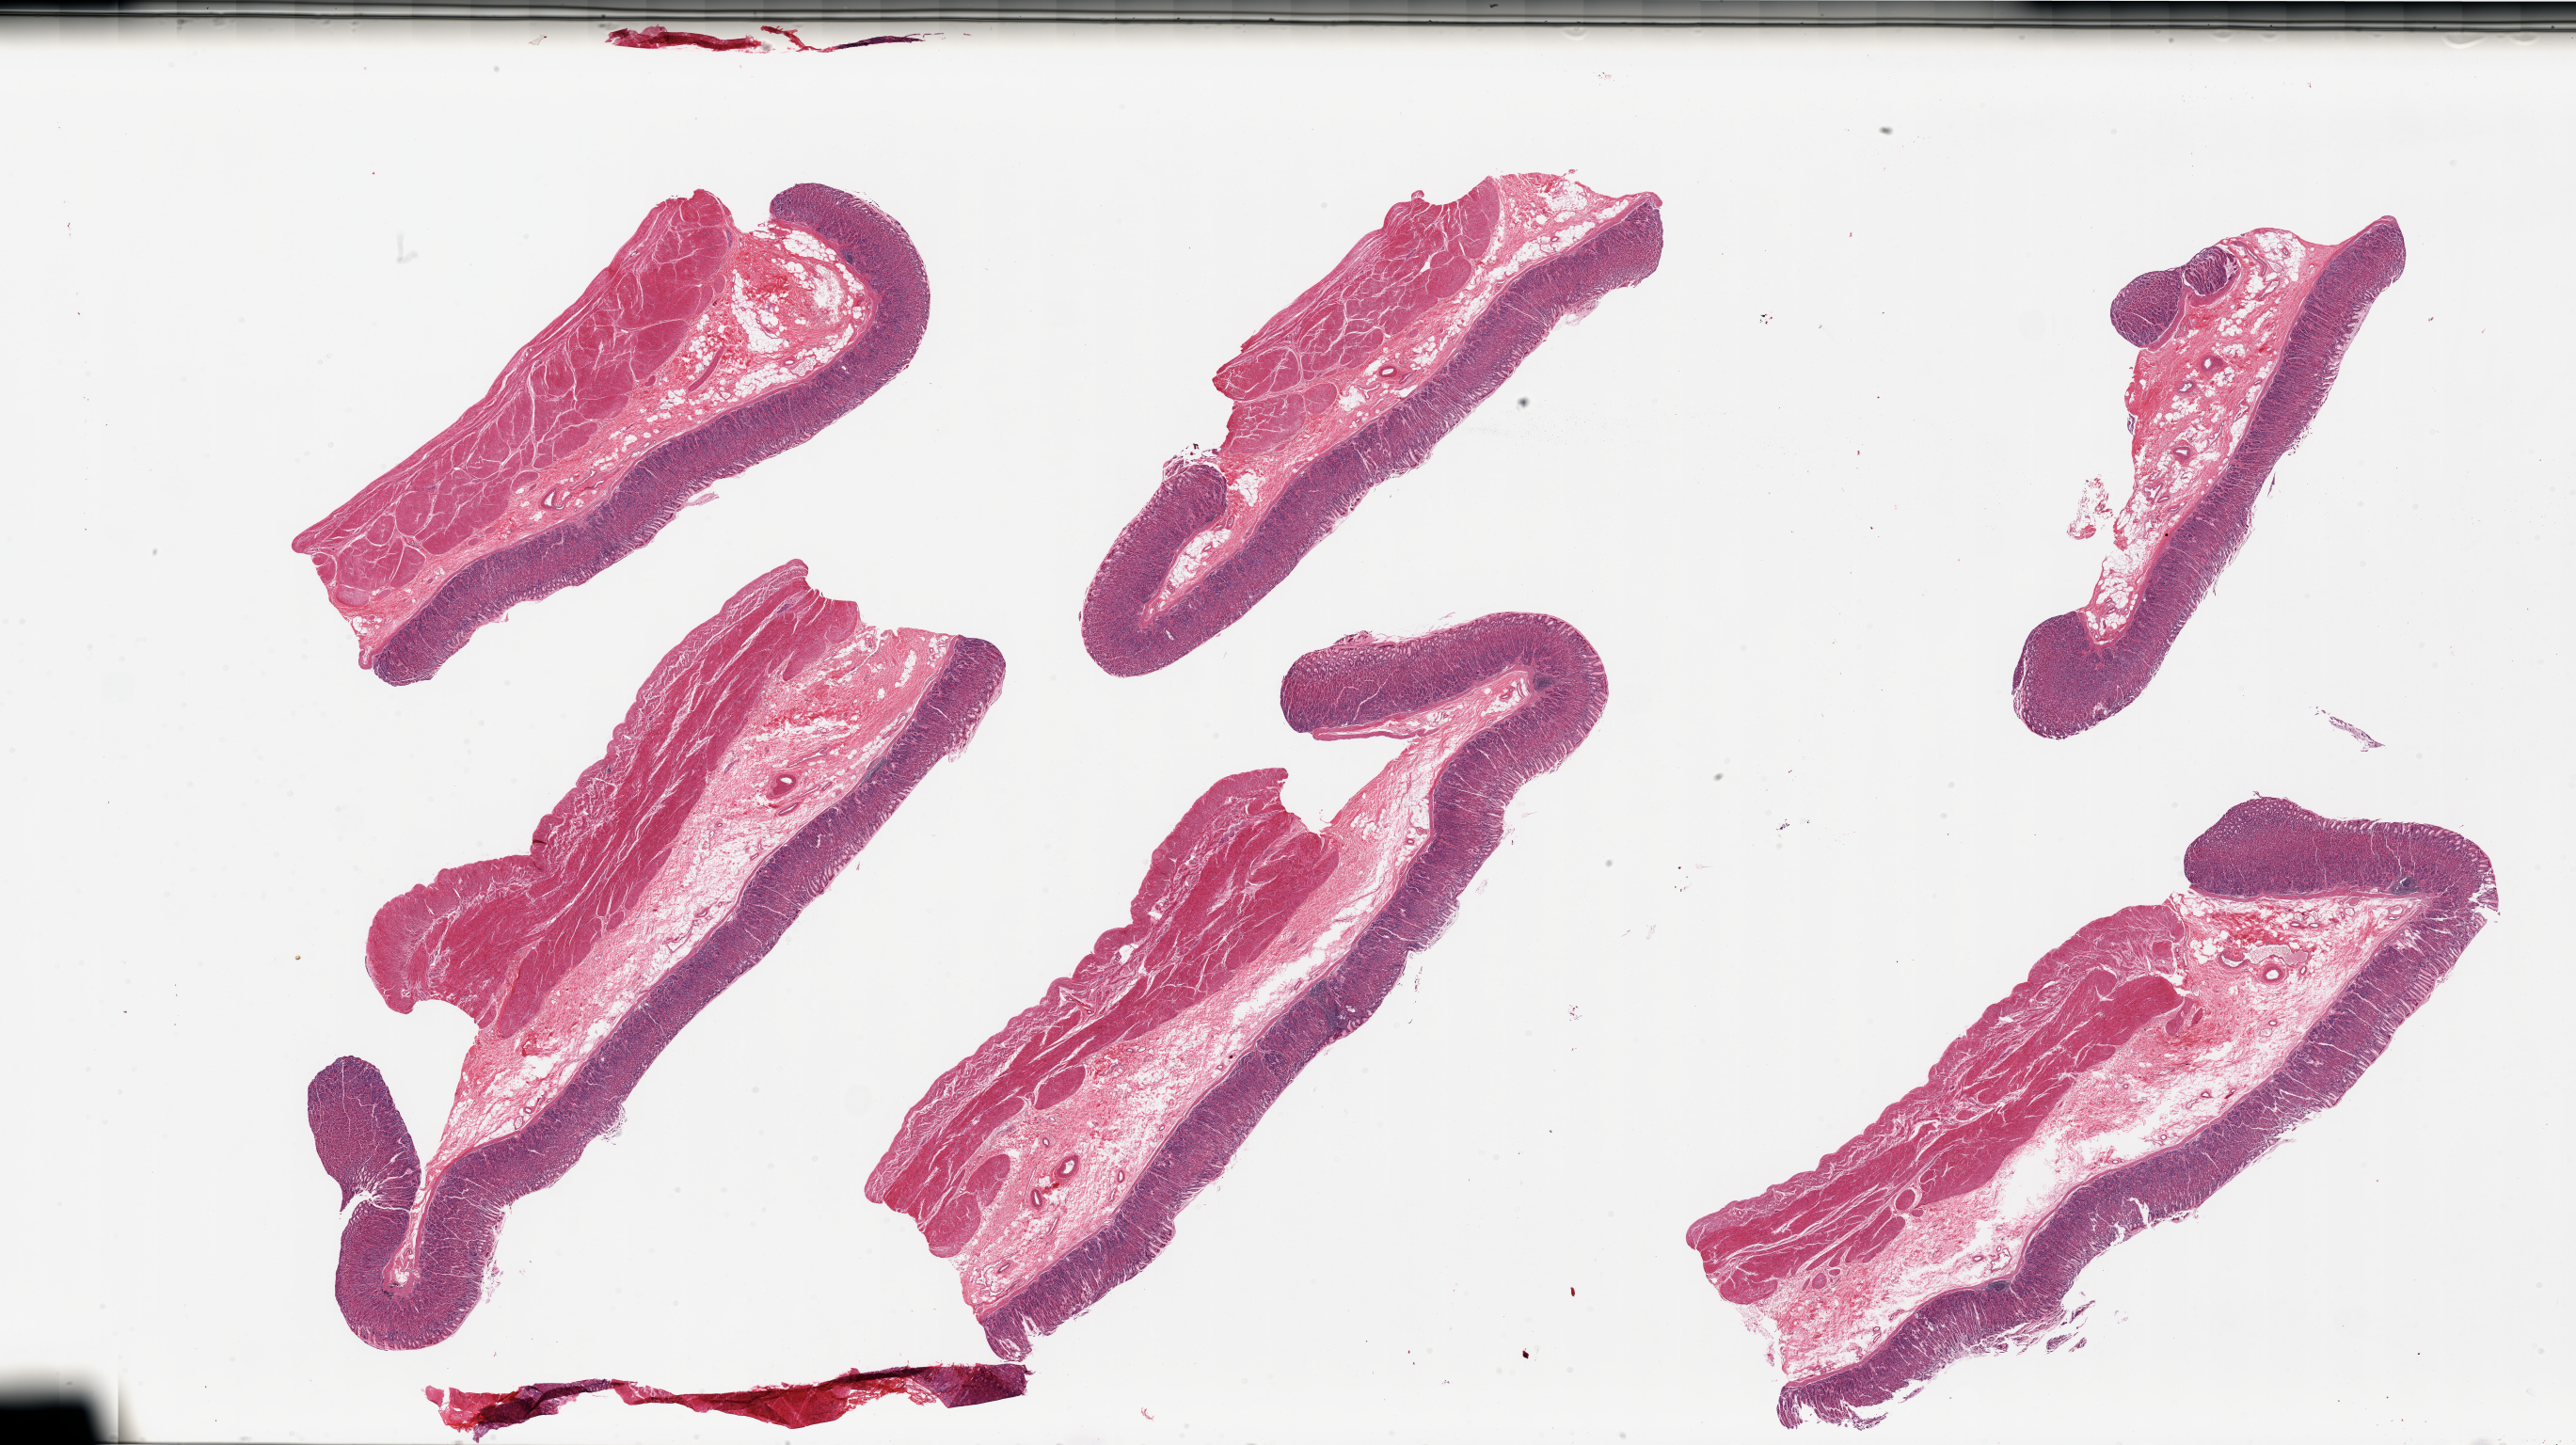
Whole-slide image, H&E stain, shown as a low-resolution overview of the whole scanned area (about 43.3 x 24.3 mm, from a 20x scan). PAXgene-fixed paraffin-embedded (PFPE) section. Target tissue: stomach. Donor tissue sample. Male donor.
- pathologist's review note for this sample: 6 pieces, well- preserved mucosa is ~1mm, ~25% thickness